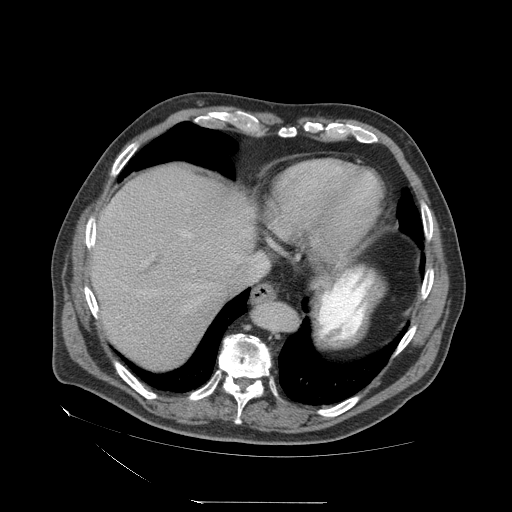
Contrast-enhanced abdominal CT (liver protocol), one axial slice. Position 59 of 83 along the scan axis. Soft-tissue window (W 400 / L 40 HU). 2.5 mm slice thickness. 512 × 512 image matrix, field of view 460 × 460 mm. From the clinical record (not read from this slice): diagnosis: hepatocellular carcinoma (patient treated with transarterial chemoembolisation; whether this scan precedes or follows treatment is not stated here); TNM stage (as recorded): Stage-I; Child-Pugh class: A; tumour differentiation: well differentiated; tumour nodularity: uninodular.
Structures marked on this image (semi-automatically segmented with operator editing):
- abdominal aorta: bounding box (x1, y1, x2, y2) in pixels: (256, 303, 297, 333)
- liver parenchyma outside the tumour (the mass and vessels are separate outlines, so this box may not span the whole liver): (91, 166, 268, 368)
- liver vessels: (108, 213, 266, 264)